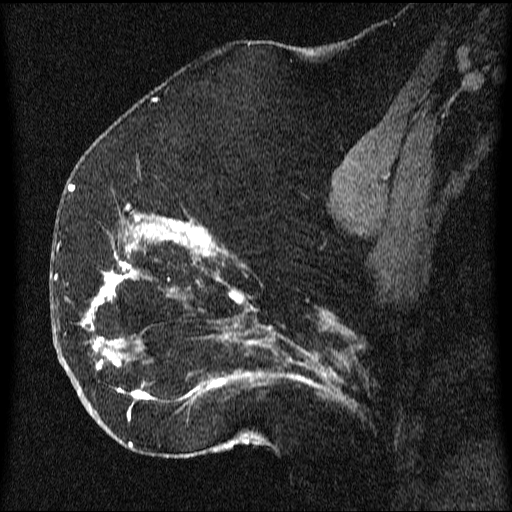
Breast MRI (dynamic contrast-enhanced), one sagittal slice. Position 29 of 64 along the scan axis. Dynamic contrast-enhanced series, image 2 of 3 at this slice position (ordered by acquisition). 1.5 T. TE 4.2 ms, TR 9.1 ms. 512 × 512 image matrix, field of view 180 × 180 mm. Patient: female, 52 years.
Structures marked on this image (semi-automatic segmentation, software-assisted and operator-edited):
- analysis volume of interest (the breast-tissue region the enhancement analysis was run in; not a lesion): bounding box (x1, y1, x2, y2) in pixels: (61, 203, 350, 438)
- tumour enhancement mask (voxels above the 70 % enhancement threshold inside the analysis volume of interest): (68, 204, 337, 422)